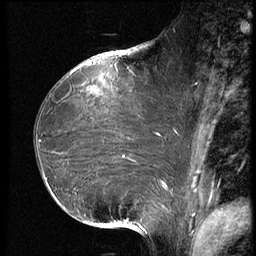
Breast MRI (dynamic contrast-enhanced), one sagittal slice. Position 37 of 66 along the scan axis. Dynamic contrast-enhanced series, image 2 of 3 at this slice position (ordered by acquisition). 1.5 T. TE 4.2 ms, TR 8.9 ms. 2.5 mm slice thickness. 256 × 256 image matrix, field of view 200 × 200 mm. Female patient, age 39 years. Case-level facts recorded for this patient, not image findings: setting: breast cancer imaged before/during neoadjuvant chemotherapy; receptor status: HER2-positive.
Outlined on this slice (semi-automatically segmented with operator editing):
- analysis volume of interest (the breast-tissue region the enhancement analysis was run in; not a lesion): bounding box <33,75,188,218> (left, top, right, bottom; pixels)
- tumour enhancement mask (voxels above the 140 % enhancement threshold inside the analysis volume of interest): <123,134,158,158>